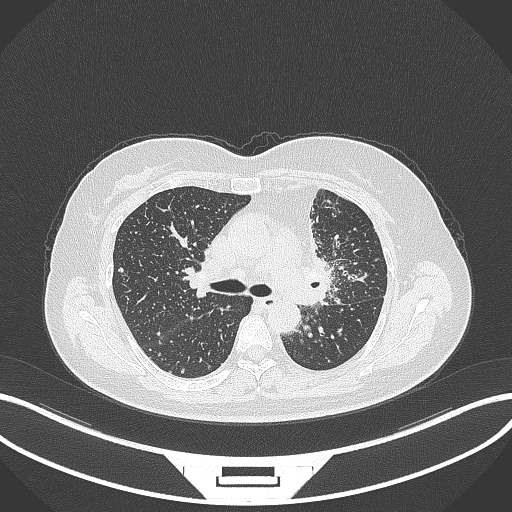
Chest CT, one axial slice; position 211 of 348 along the scan axis; reconstruction kernel B70f; 120 kVp; lung window (W 1500 / L -600 HU); 1 mm slice thickness; 512 × 512 image matrix, field of view 400 × 400 mm. Patient: female, 49 years. Case-level facts recorded for this patient, not image findings: clinical TNM (as recorded): T1c N0 M1.
Annotated regions visible in this slice (bounding box drawn by a radiologist):
- lung tumour (recorded histology: adenocarcinoma): bounding box [x1, y1, x2, y2] px = [296, 250, 338, 308]